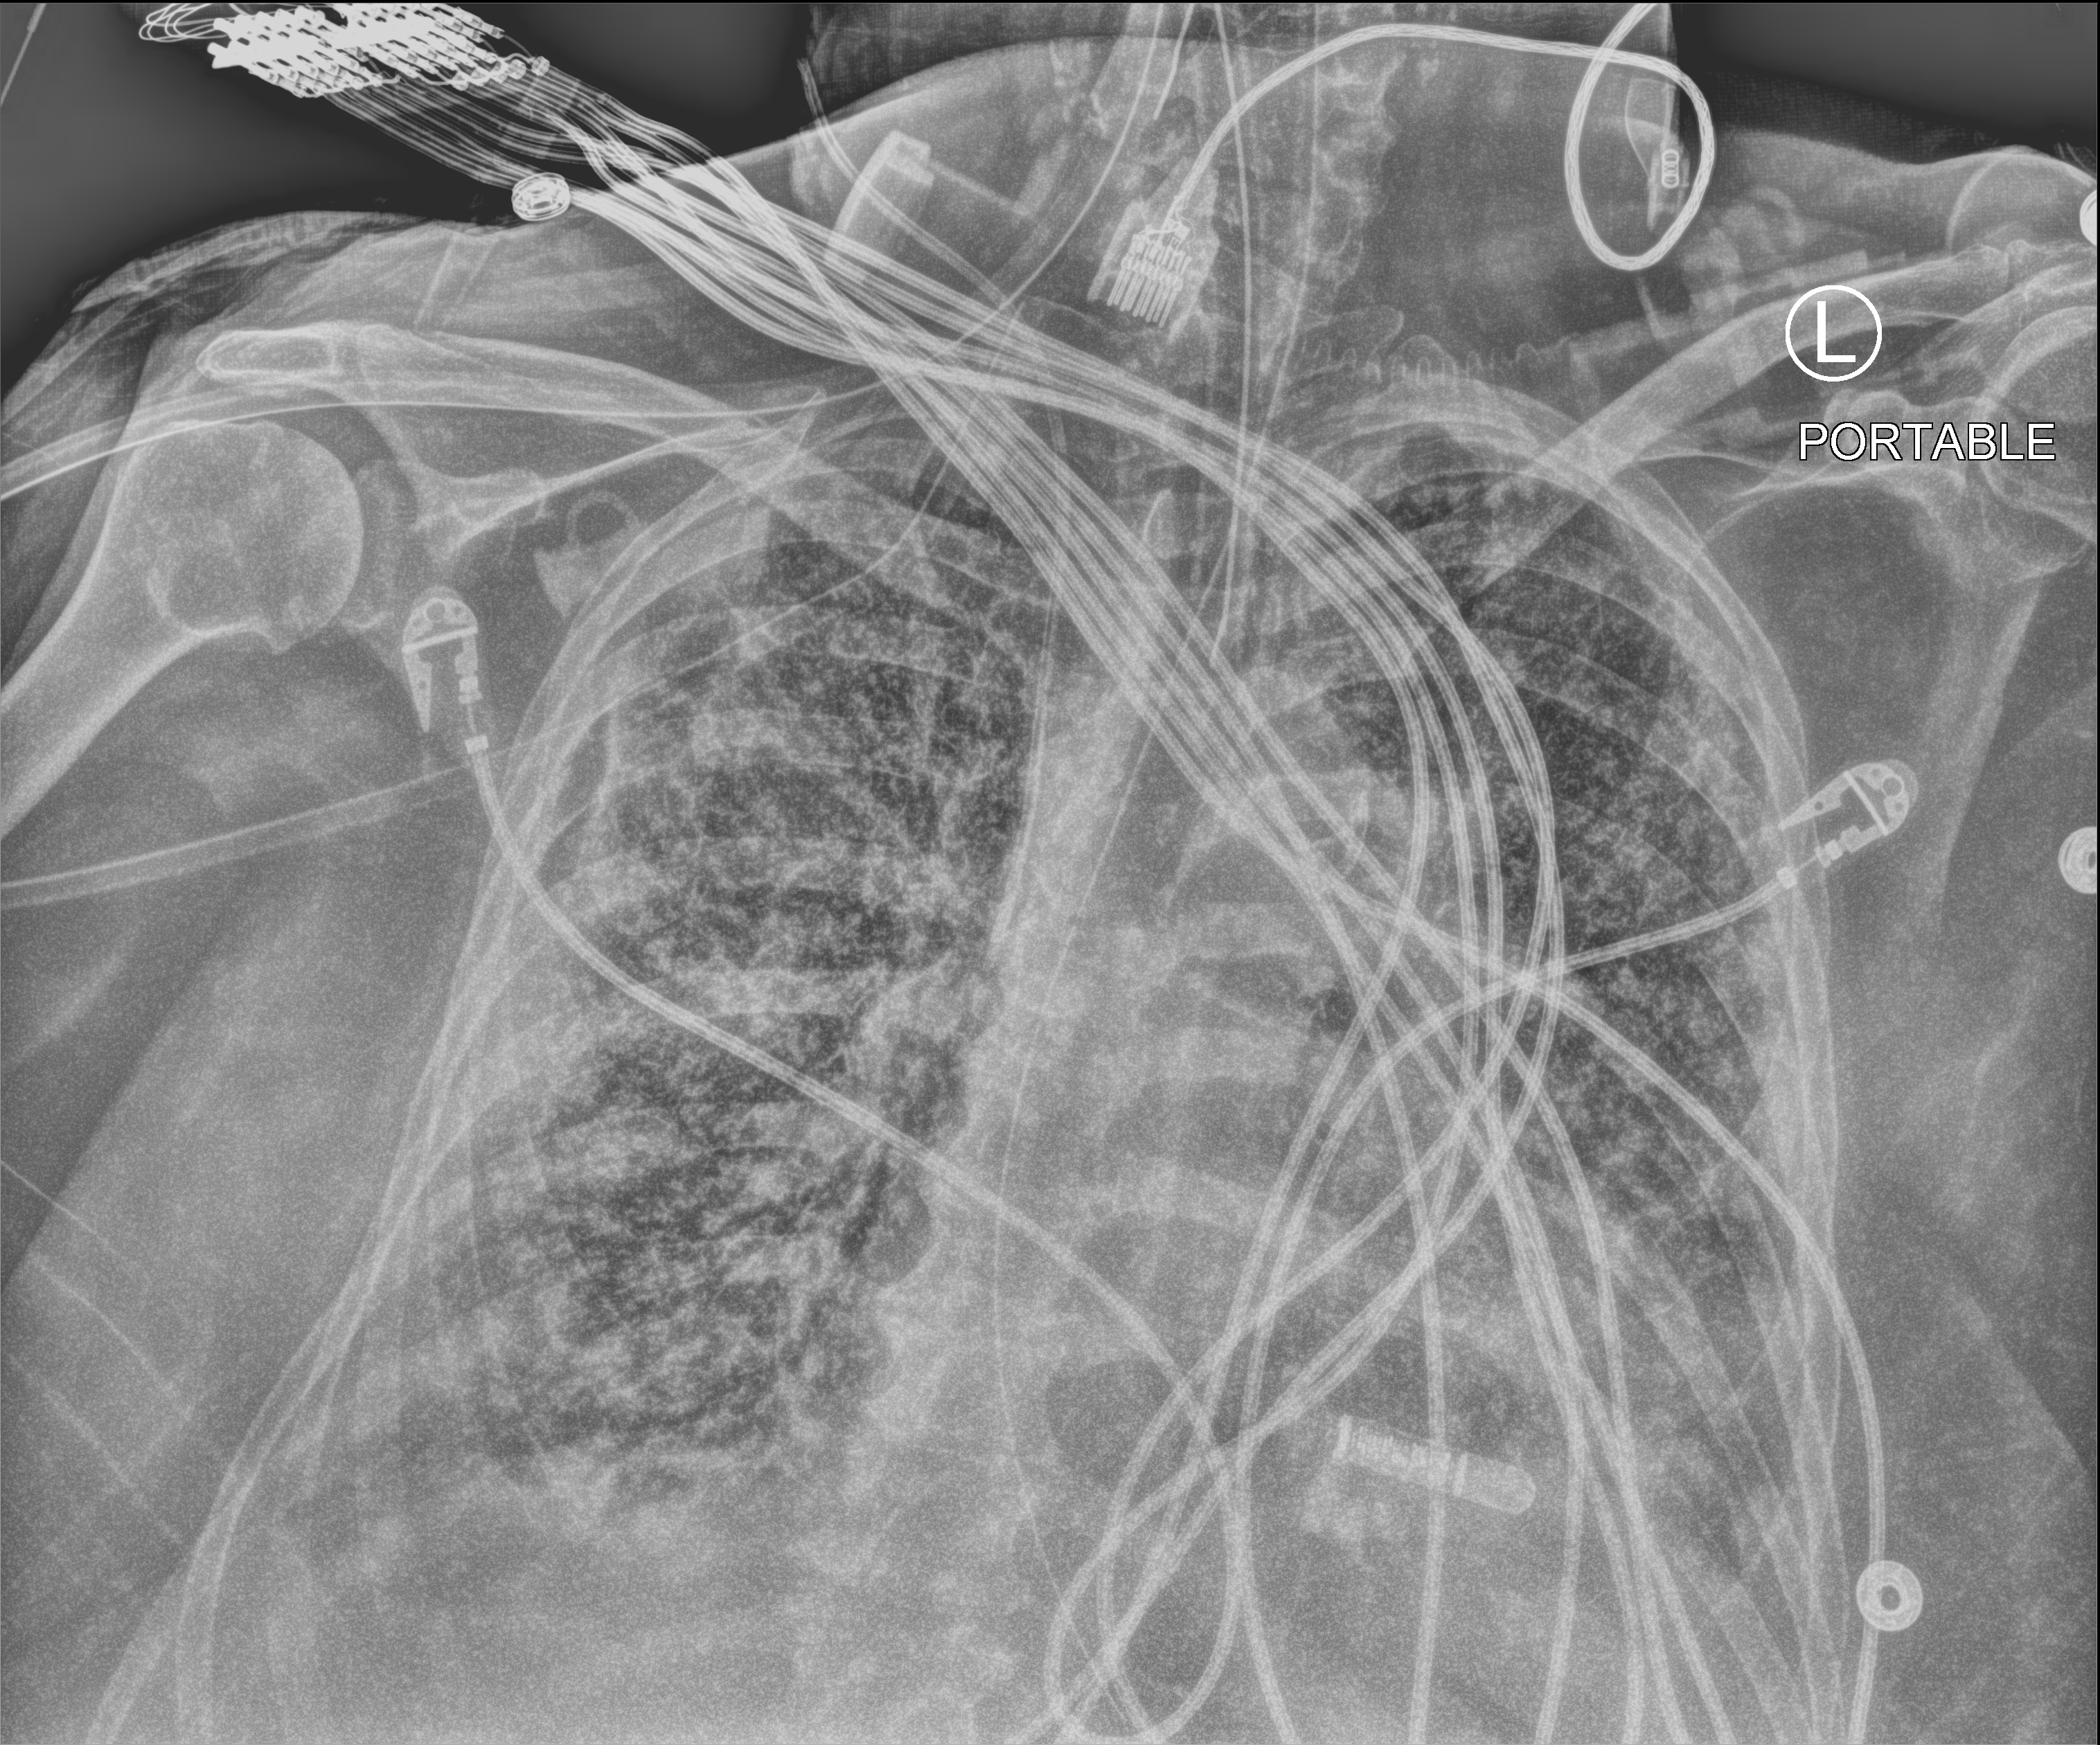
Bedside chest radiograph (computed radiography); anteroposterior (AP) projection. Female patient hospitalised with COVID-19, age 60–74 years.
Admission-level facts for this patient (not findings on this image; timing relative to this image not recorded): smoking status (admission record): former; mechanically ventilated during this hospital stay: yes; hypertension (admission record): yes.